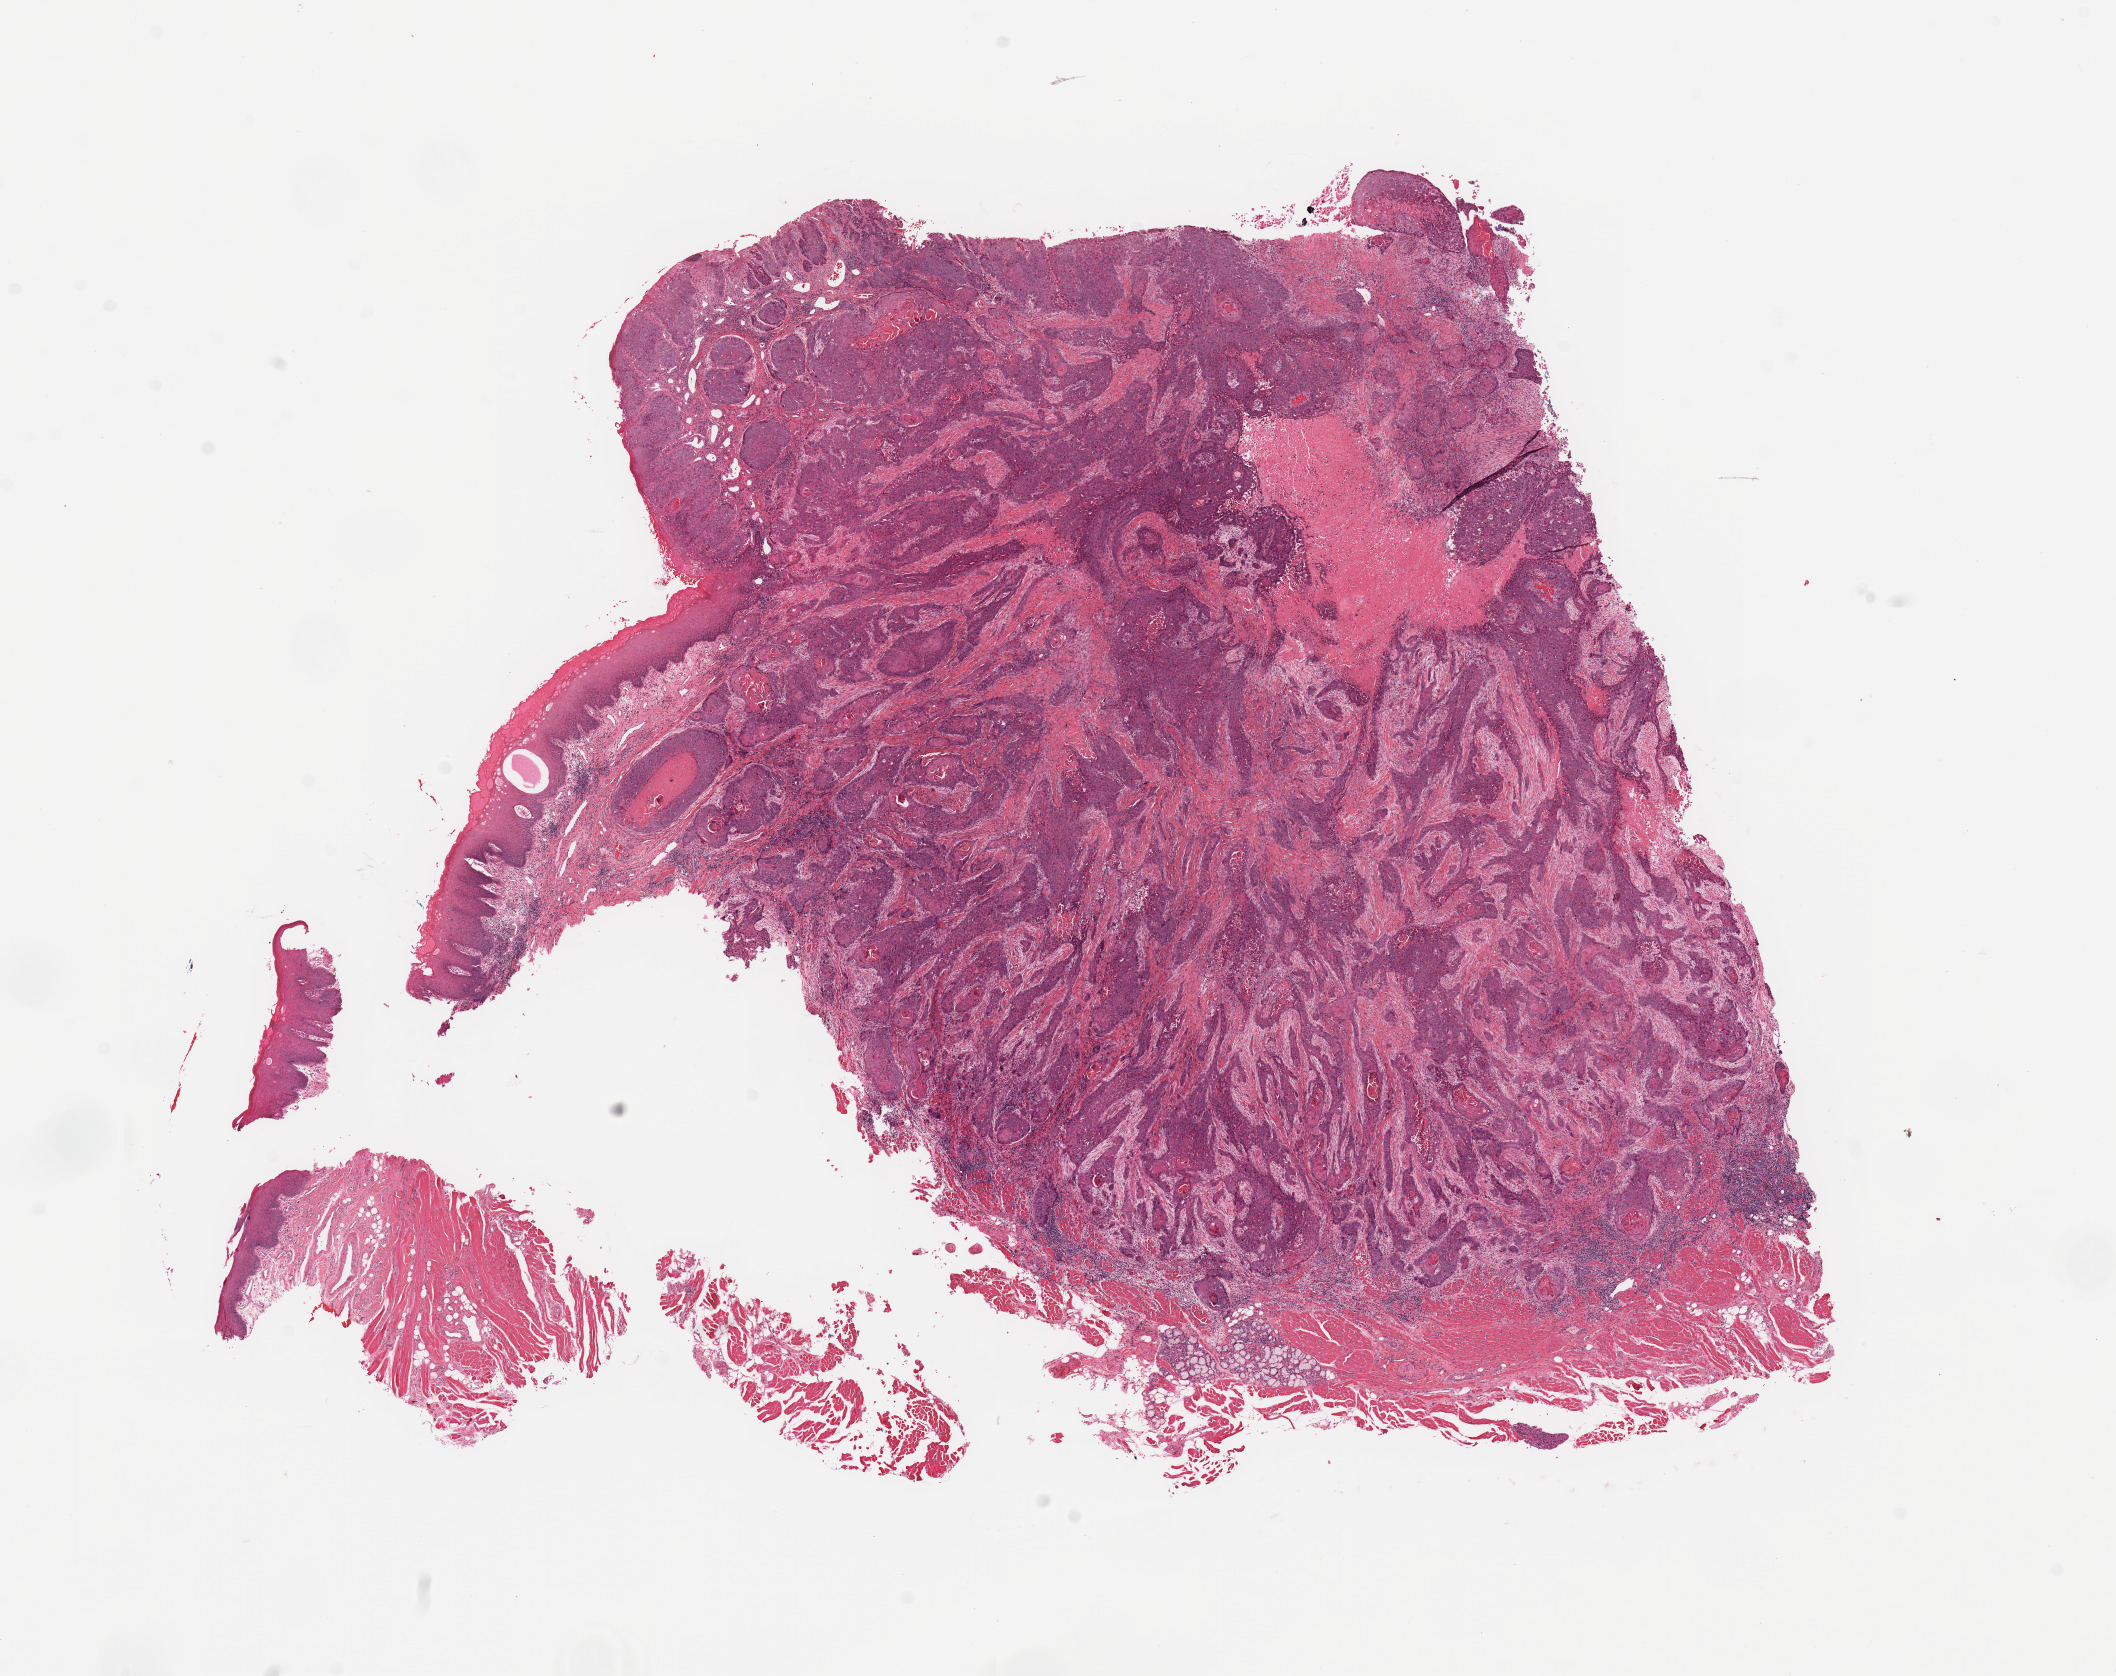
Whole-slide histology image, H&E-stained — low-resolution overview of the scanned area, about 16.7 x 13.3 mm. Tumour tissue sample, sampled site: floor of mouth. Male, 57 y/o. Histologic grade: G2 (moderately differentiated). Pathologist review of this section (percent, as recorded): tumour nuclei 80%, necrosis 7%.
Primary tumour site (as recorded): oral cavity. Histologic diagnosis: Squamous cell carcinoma, NOS (floor of mouth, NOS). AJCC pathologic stage: IVA.